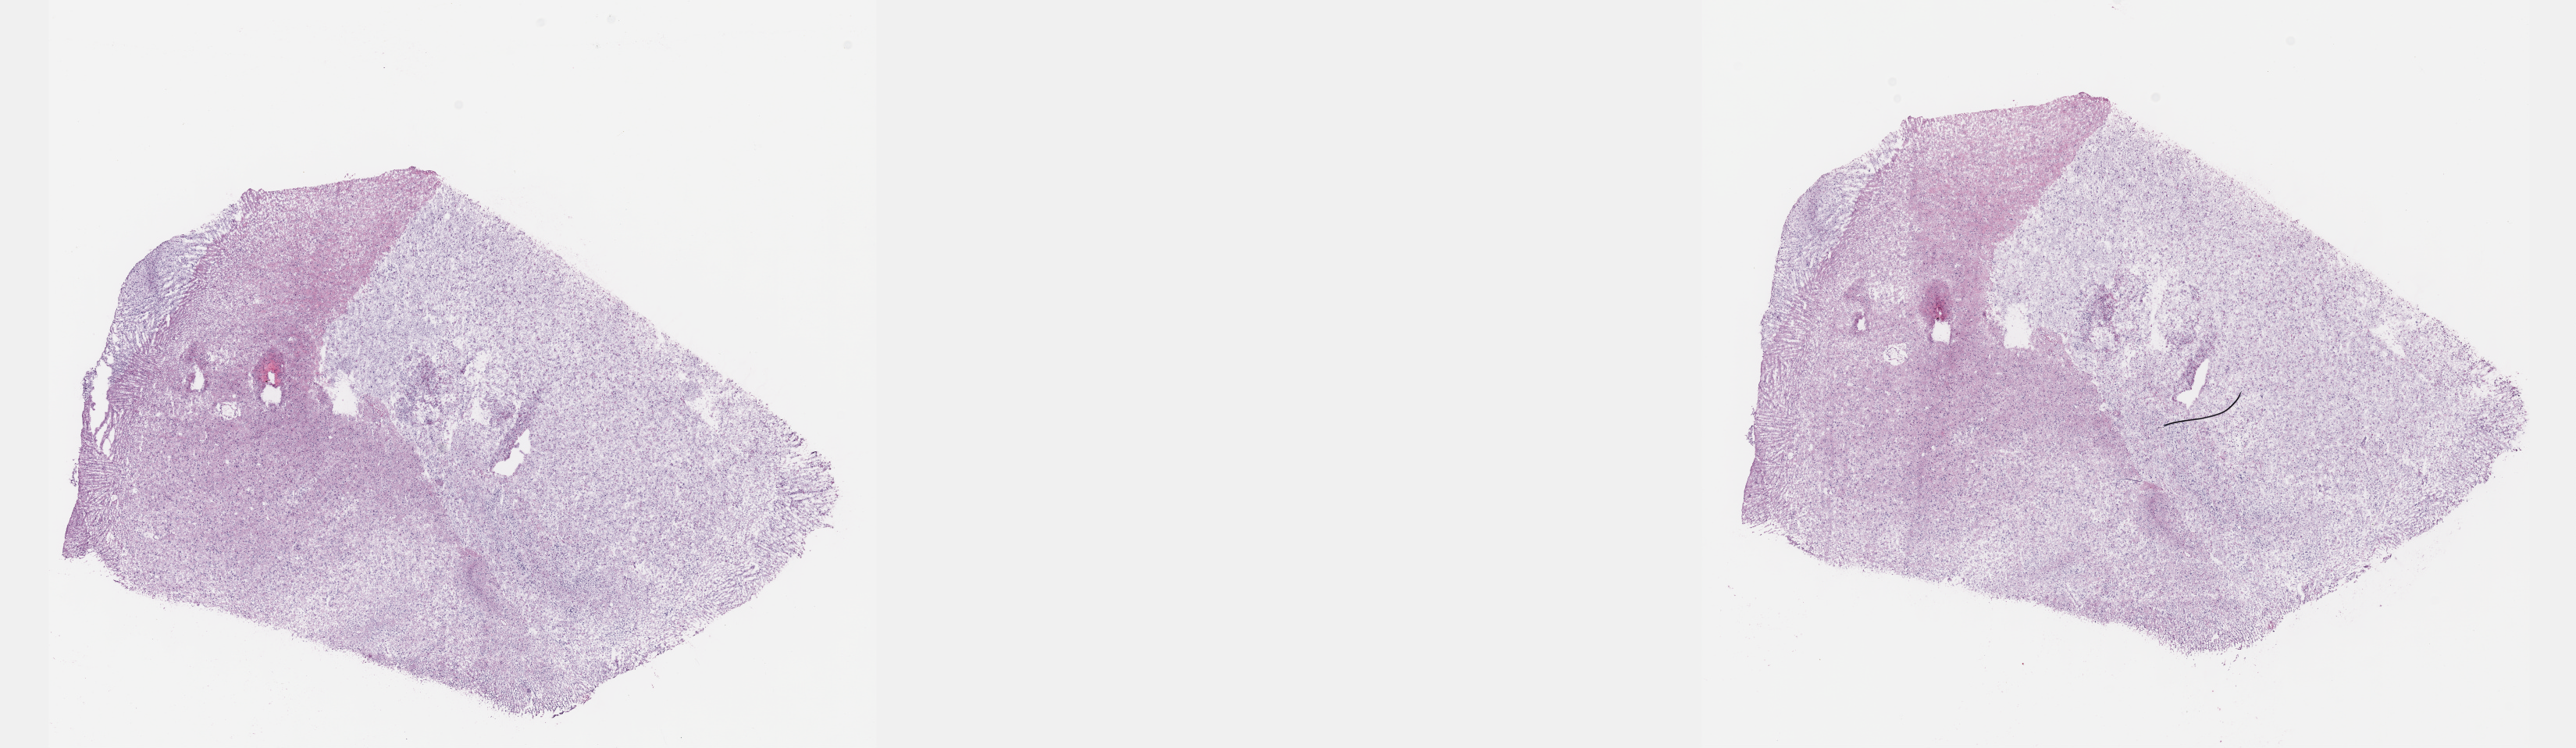
Whole-slide histology image, H&E, whole scanned area (about 26.7 x 7.7 mm, slide scanned at 40x) shown as a low-resolution overview, frozen section from the top of the tissue portion, sample: primary tumour, brain. Patient: male, age at initial diagnosis 39 years. Histologic grade: G2 (moderately differentiated). Composition of this section per pathologist review: tumour cells 50%, tumour nuclei 90%, normal cells 10%, stromal cells 40%, necrosis 0%. Inflammatory infiltration, as recorded: lymphocyte infiltration 0%, monocyte infiltration 0%, neutrophil infiltration 0%.
- histologic diagnosis: Mixed glioma (cerebrum)
- laterality: right